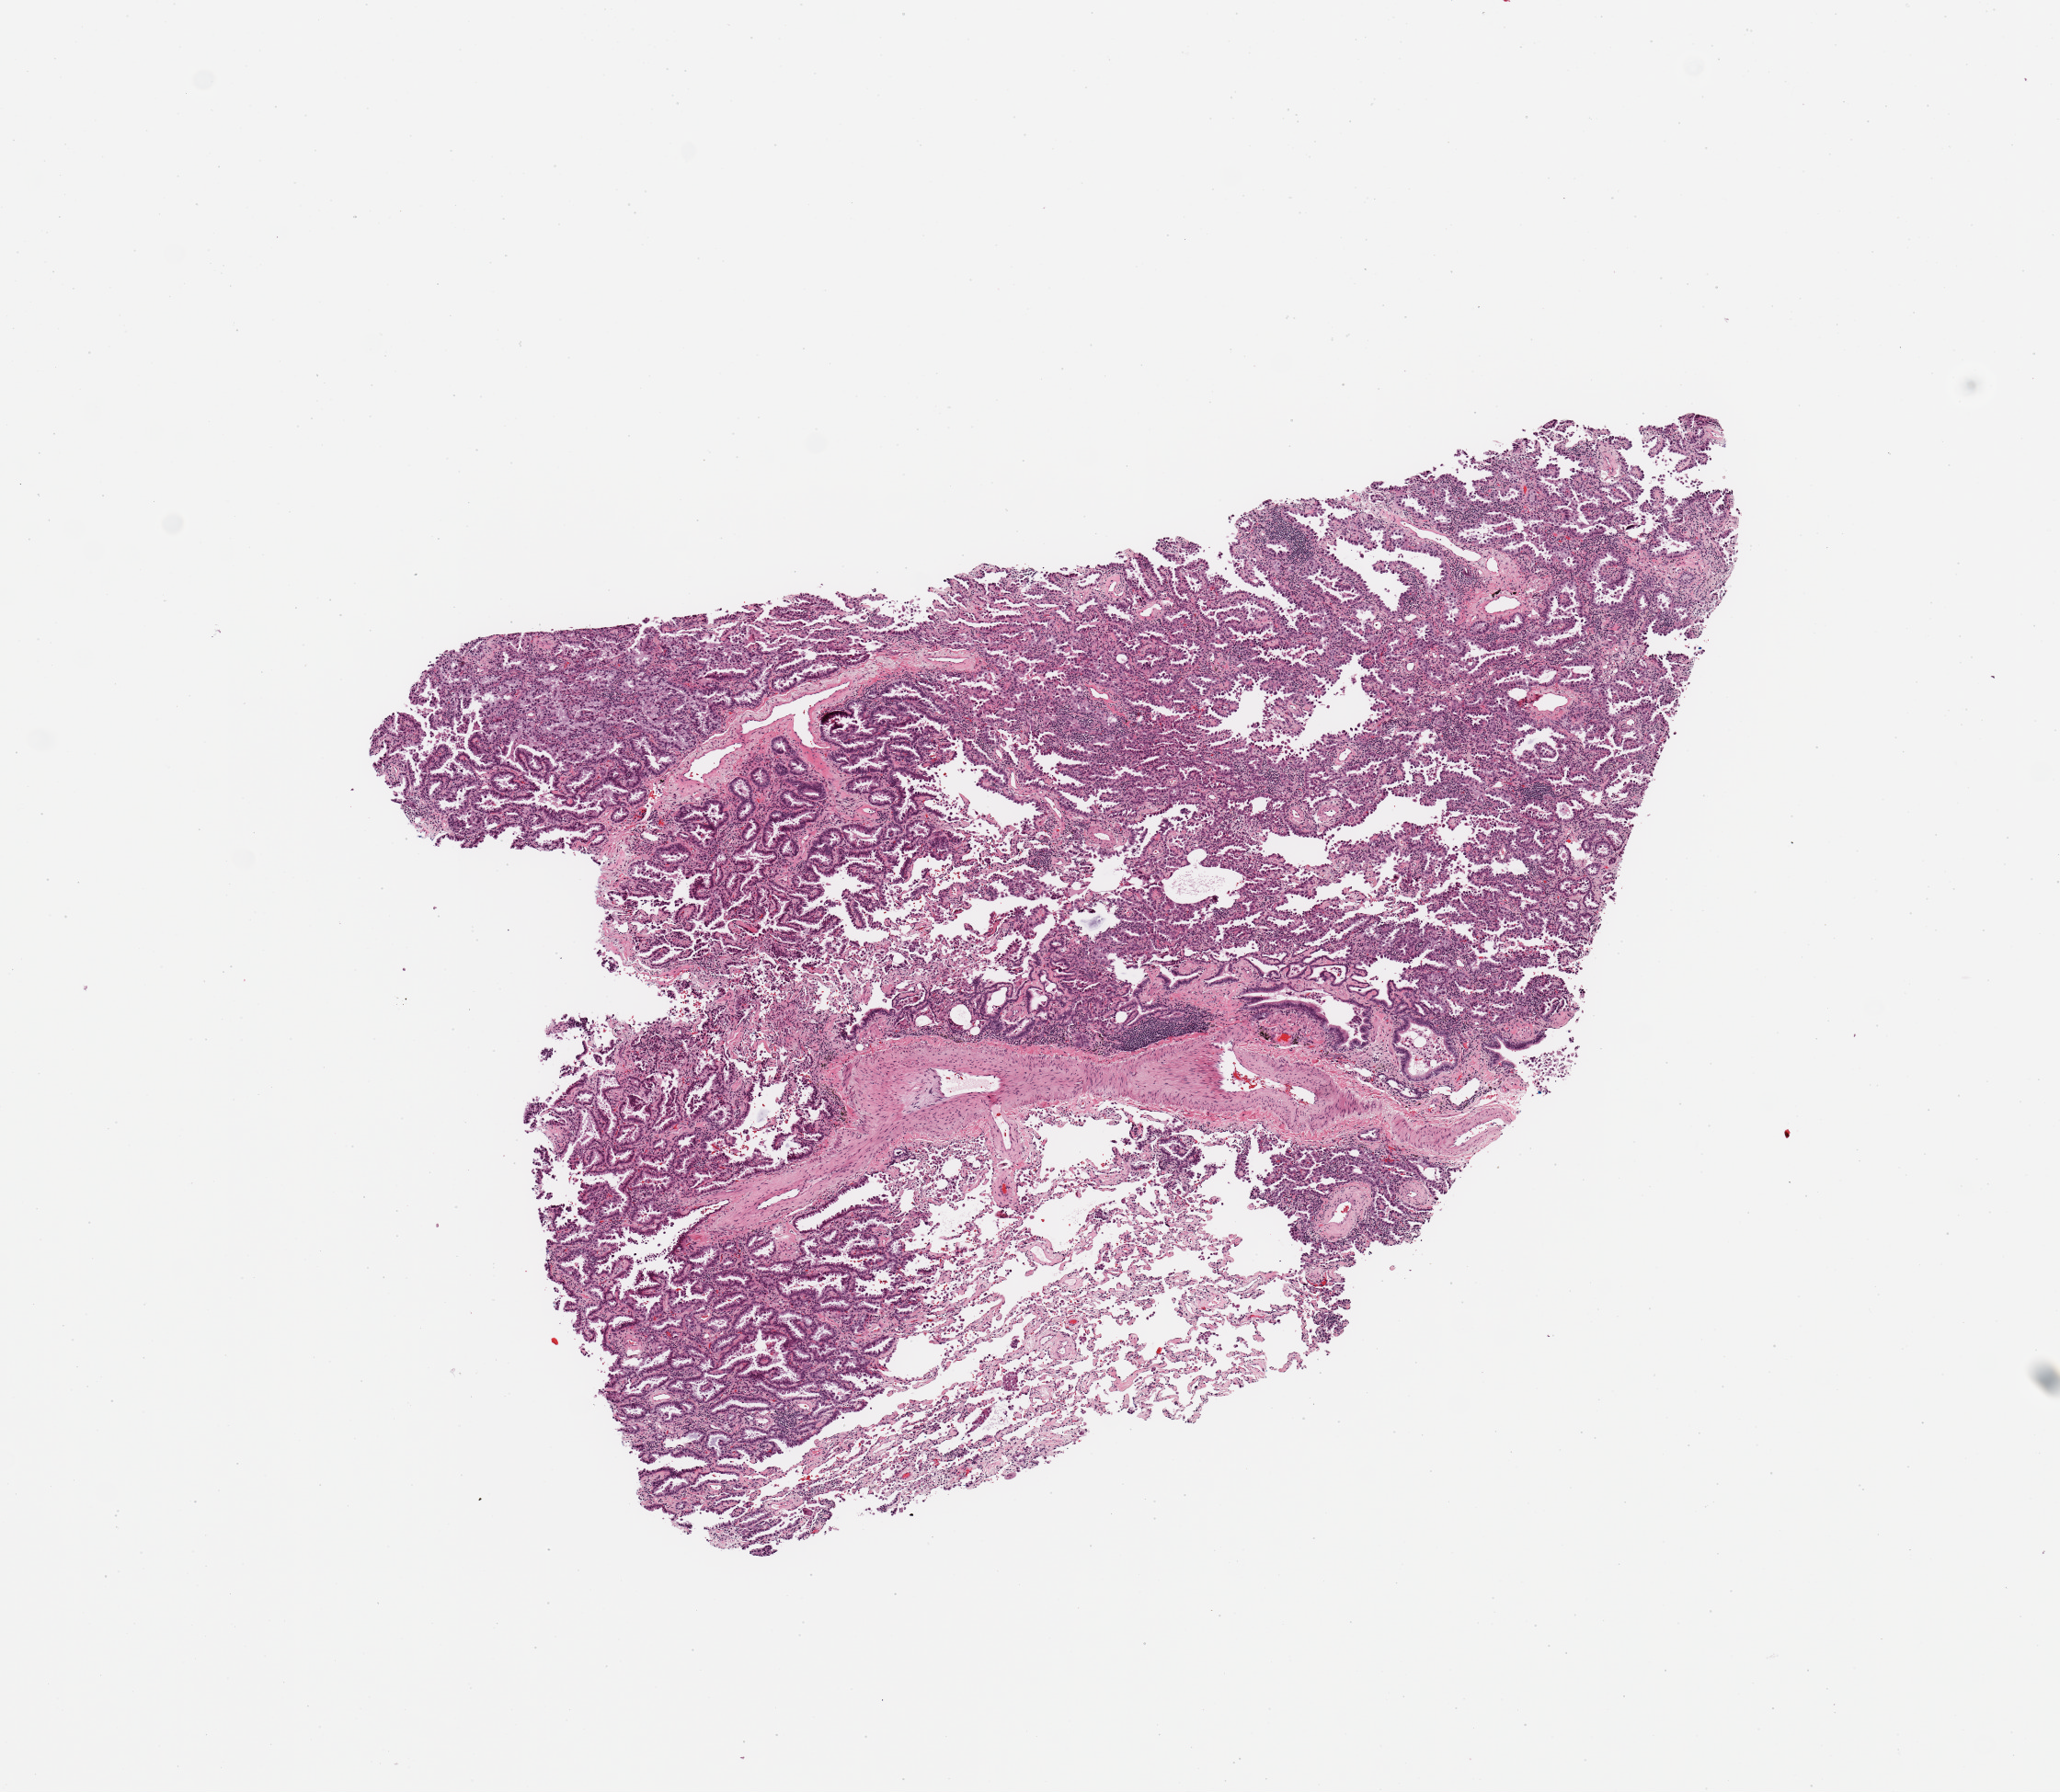
Digitized H&E-stained tissue section (whole slide) — a low-resolution overview of the entire scanned area, about 8.9 x 7.7 mm (acquisition: 20x scan); tumour tissue sample, lung. Patient: male, age 77 years. Histologic grade: G2 (moderately differentiated).
• AJCC pathologic stage: IIIA
• diagnosis: Adenocarcinoma, NOS
• primary tumour site (as recorded): right lower lobe